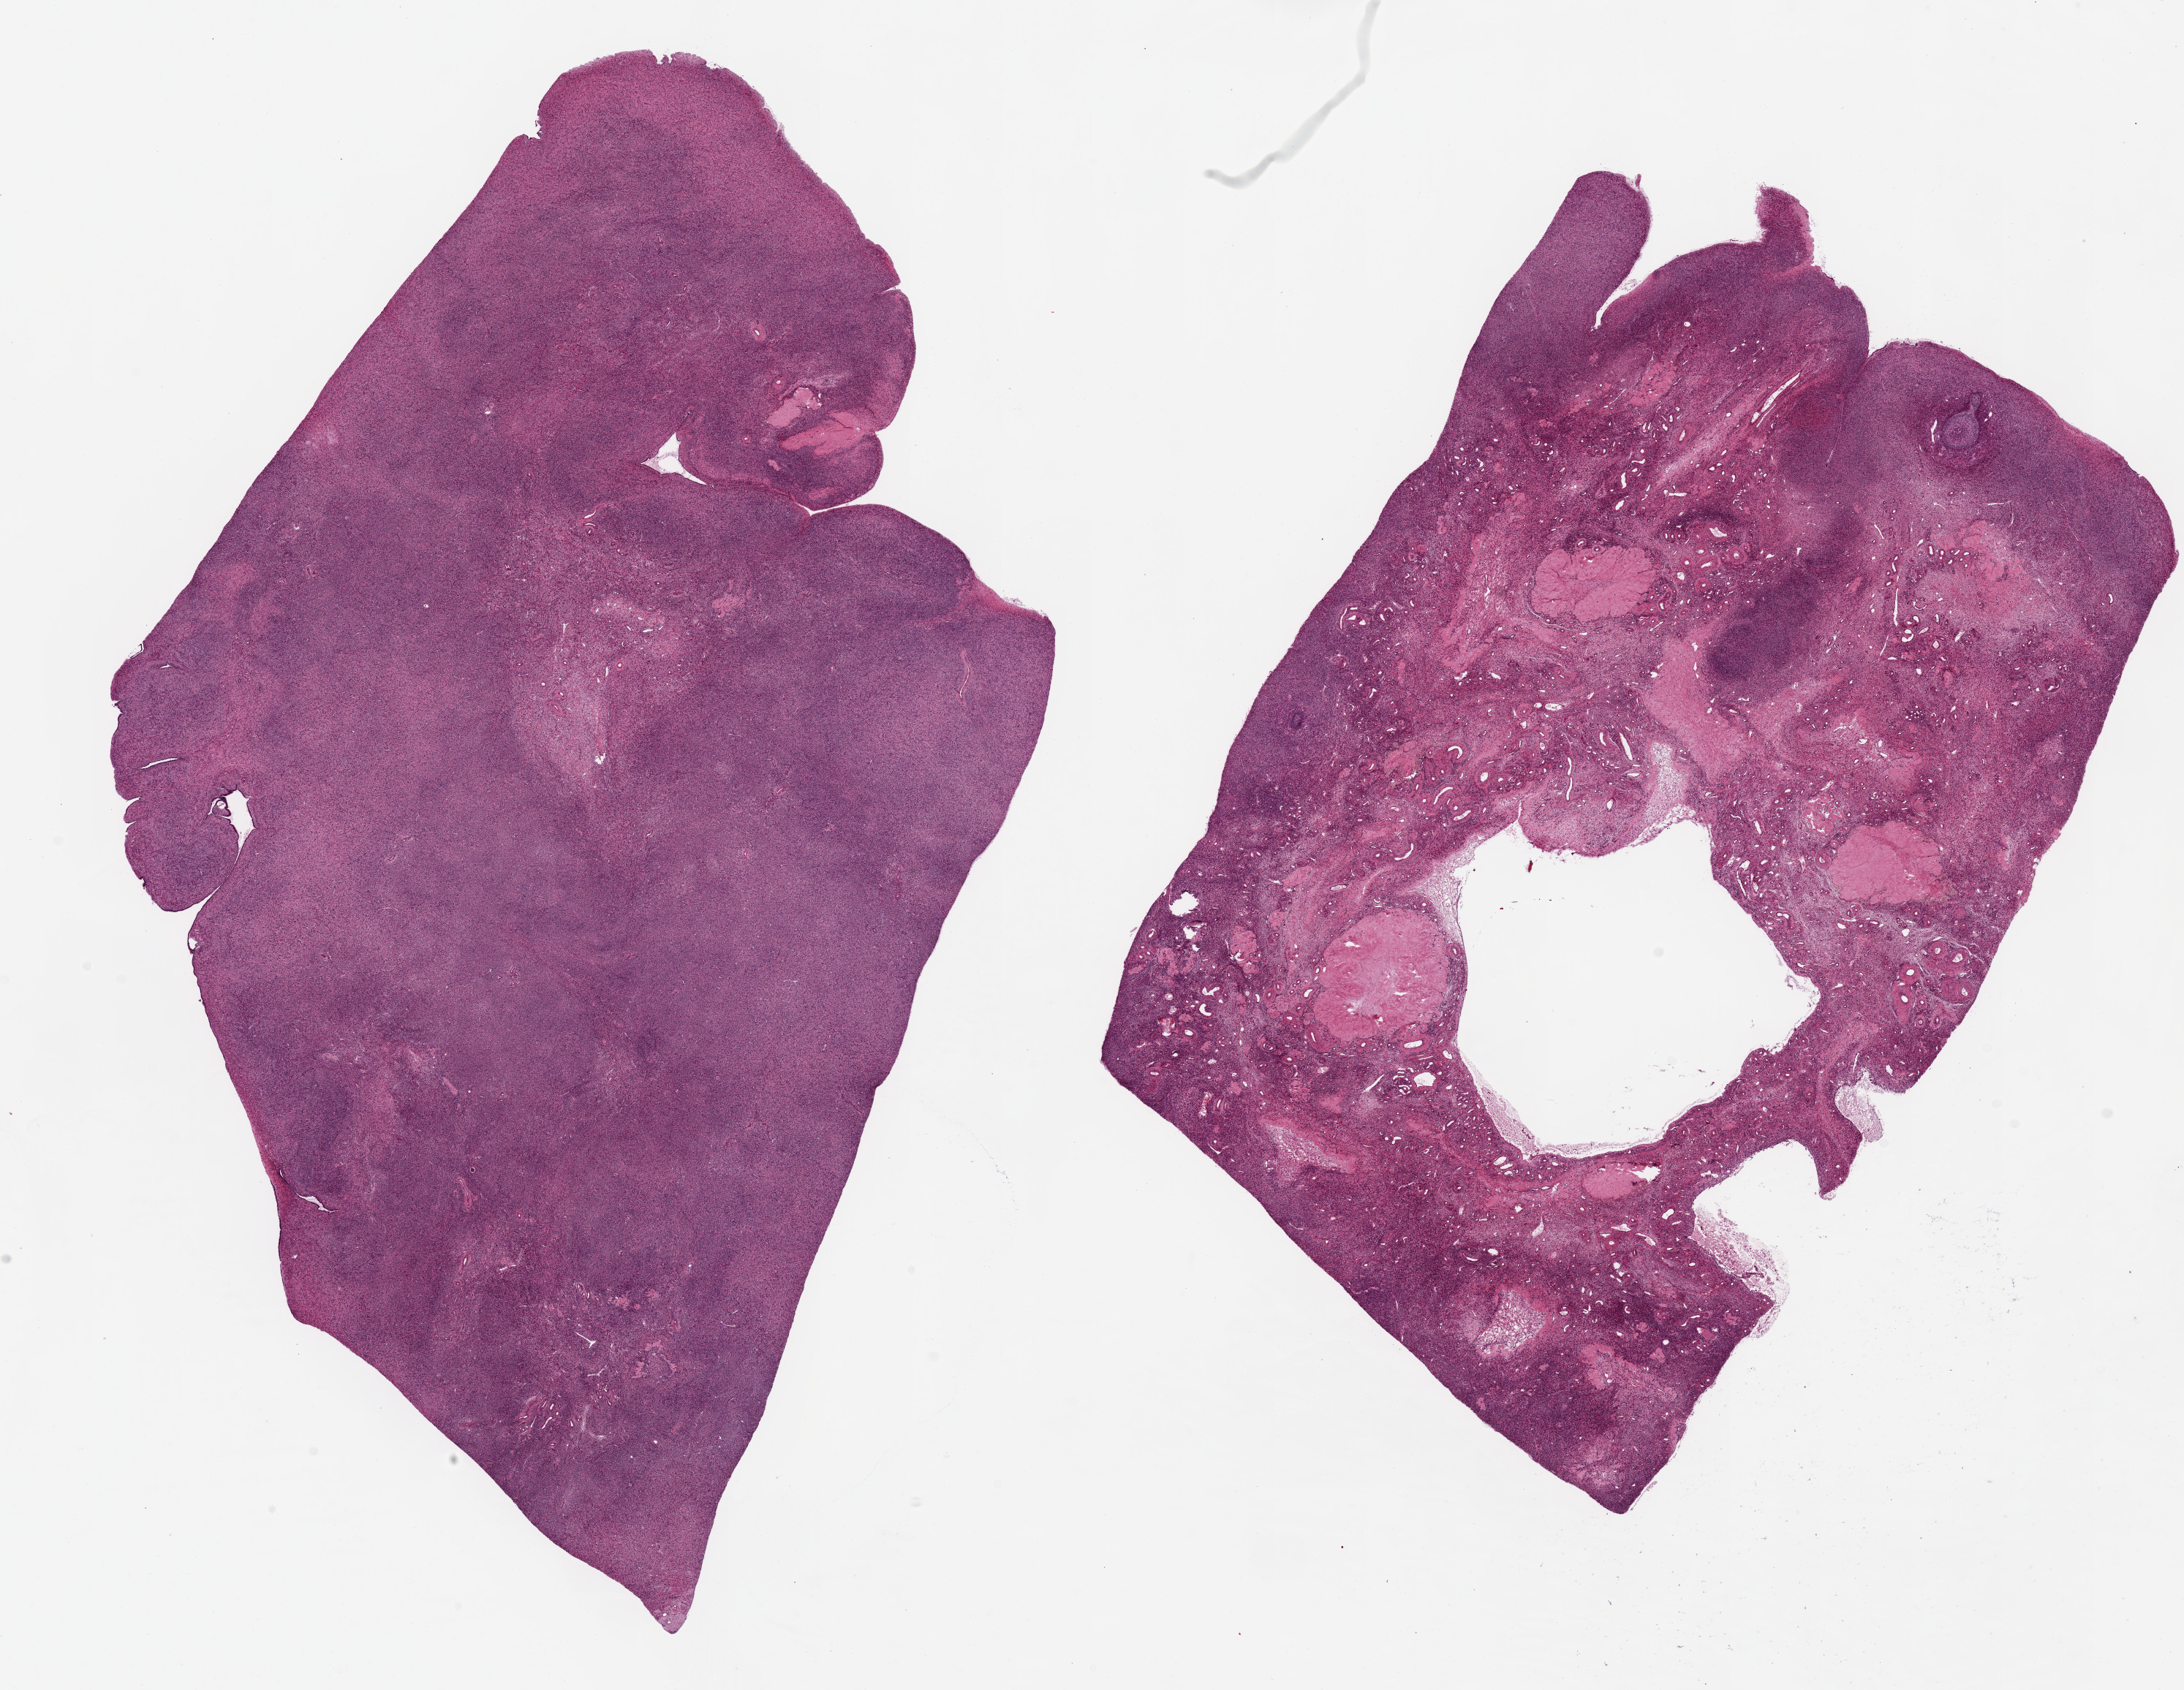
Haematoxylin and eosin whole-slide image — whole scanned area (about 23.6 x 18.3 mm, acquisition: 20x scan) shown as a low-resolution overview, PAXgene-fixed, paraffin-embedded tissue, target tissue: ovary, tissue donor sample. Female donor.
Review note (as recorded): 2 ~ 15x11mm aliquots. Corpora albicantia and an occasional ovum noted.